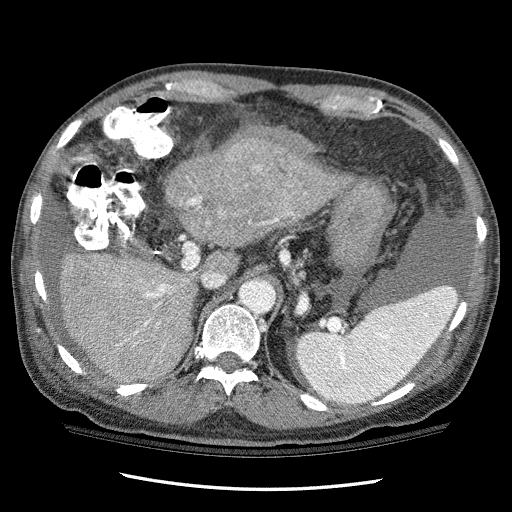
Contrast-enhanced abdominal CT (liver protocol), one axial slice. Slice 71 of 114 in the series (ordered by position). Reconstruction kernel STANDARD. 120 kVp. One of 3 acquisitions stored at this slice position. Soft-tissue window (W 400 / L 40 HU). 2.5 mm slice thickness. 512 × 512 image matrix. Case-level facts recorded for this patient, not image findings: diagnosis: hepatocellular carcinoma (patient treated with transarterial chemoembolisation; whether this scan precedes or follows treatment is not stated here); TNM stage (as recorded): Stage-I; Child-Pugh class: C; tumour differentiation: well differentiated; tumour nodularity: uninodular.
Annotated regions visible in this slice (semi-automatically segmented with operator editing):
- liver parenchyma outside the tumour (the mass and vessels are separate outlines, so this box may not span the whole liver): bounding box (x1, y1, x2, y2) in pixels: (58, 150, 353, 382)
- mass: (224, 125, 325, 174)
- liver vessels: (120, 196, 293, 345)